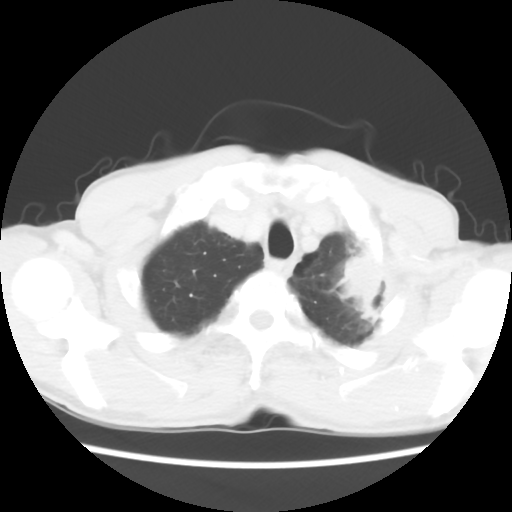
Chest CT, one axial slice. Slice 53 of 60 in the series (ordered by position). Lung window (W 1500 / L -600 HU). 512 × 512 image matrix, field of view 308 × 308 mm. Patient: male, 64 years. From the clinical record (not read from this slice): clinical TNM (as recorded): T3 N3 M0.
Annotated regions visible in this slice (bounding box drawn by a radiologist):
- lung tumour (recorded histology: adenocarcinoma): bounding box [x1, y1, x2, y2] px = [331, 240, 393, 330]